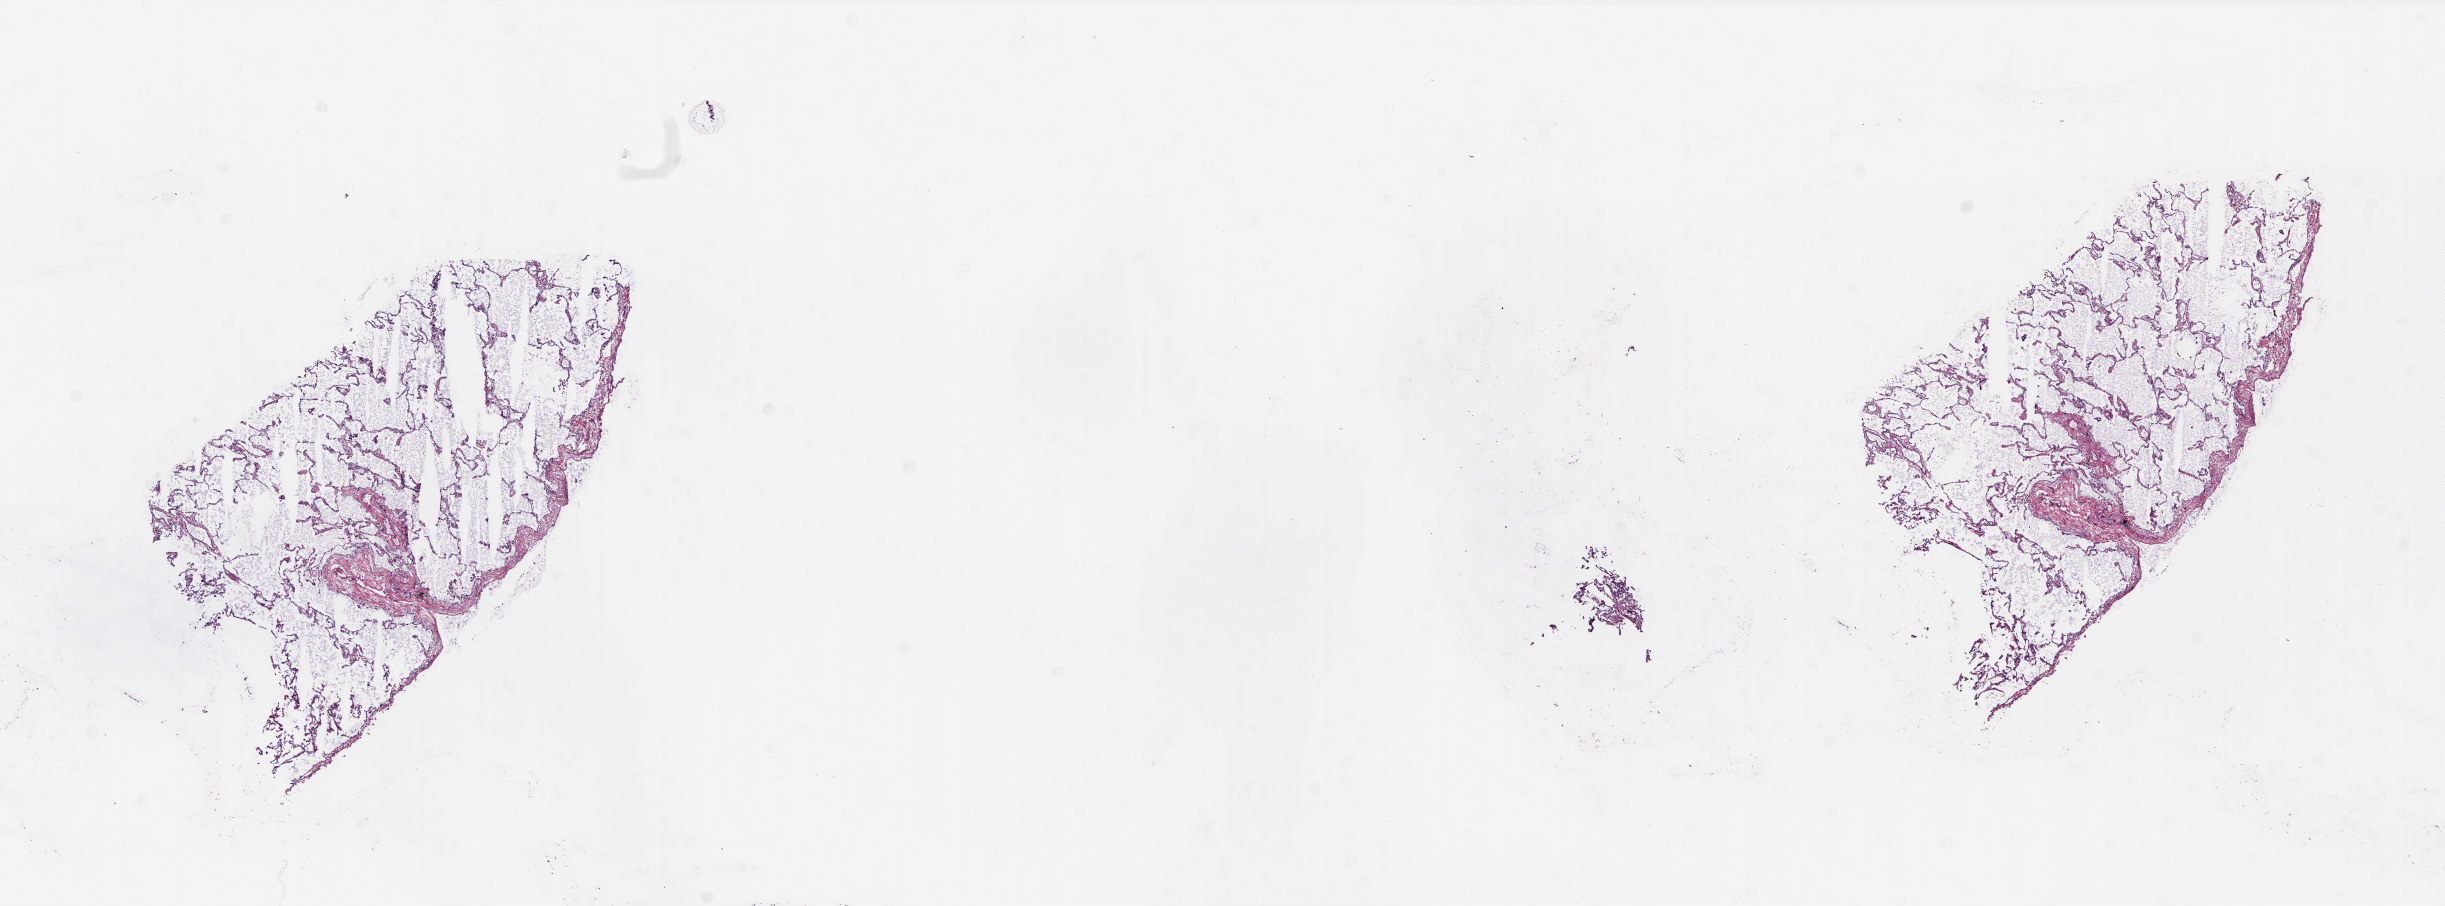
Digitized Hematoxylin and eosin (H&E) stained tissue section (whole slide) — shown as a low-resolution overview of the whole scanned area (about 19.7 x 7.3 mm, acquisition: 20x scan); frozen section from the top of the tissue portion; lung, solid tissue normal (non-tumour tissue) sample. Female, age 72 years at initial diagnosis. Slide review estimates, as recorded: tumour cells 0%, tumour nuclei 0%, normal cells 100%, stromal cells 0%, necrosis 0%. Inflammatory infiltration, as recorded: lymphocyte infiltration 40%, monocyte infiltration 20%, neutrophil infiltration 20%.
This section: solid tissue normal sample (biorepository sample class). Patient diagnosis: Adenocarcinoma, NOS (upper lobe, lung).